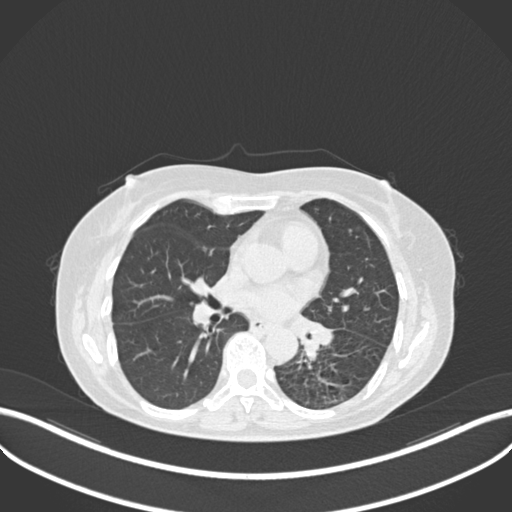
Chest CT, one axial slice. Position 131 of 270 along the scan axis. Reconstruction kernel B30f. 120 kVp. Lung window (W 1500 / L -600 HU). 1 mm slice thickness. 512 × 512 image matrix, field of view 400 × 400 mm. Patient: female, 63 years. Case-level facts recorded for this patient, not image findings: clinical TNM (as recorded): T1b N0 M0; histopathological grade: G2-3.
Structures marked on this image (rectangle marked by the reading radiologist):
- lung tumour (recorded histology: adenocarcinoma): bounding box [x1, y1, x2, y2] px = [293, 314, 338, 361]